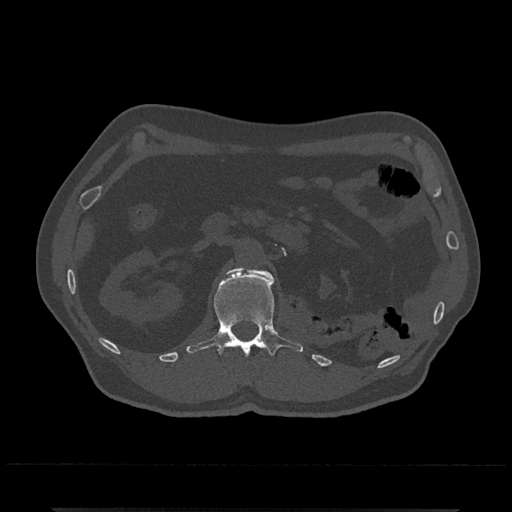
CT including the spine, one axial slice; slice 360 of 797 in the series (ordered by position); 120 kVp; bone window (W 1800 / L 400 HU); 0.5 mm slice thickness; 512 × 512 image matrix, field of view 393 × 393 mm. Male patient, age 67 years. Case-level facts recorded for this patient, not image findings: primary cancer: prostate.
Annotated regions visible in this slice (semi-automatic segmentation, software-assisted and operator-edited):
- L1 vertebra: bounding box [x1, y1, x2, y2] px = [186, 267, 303, 357]